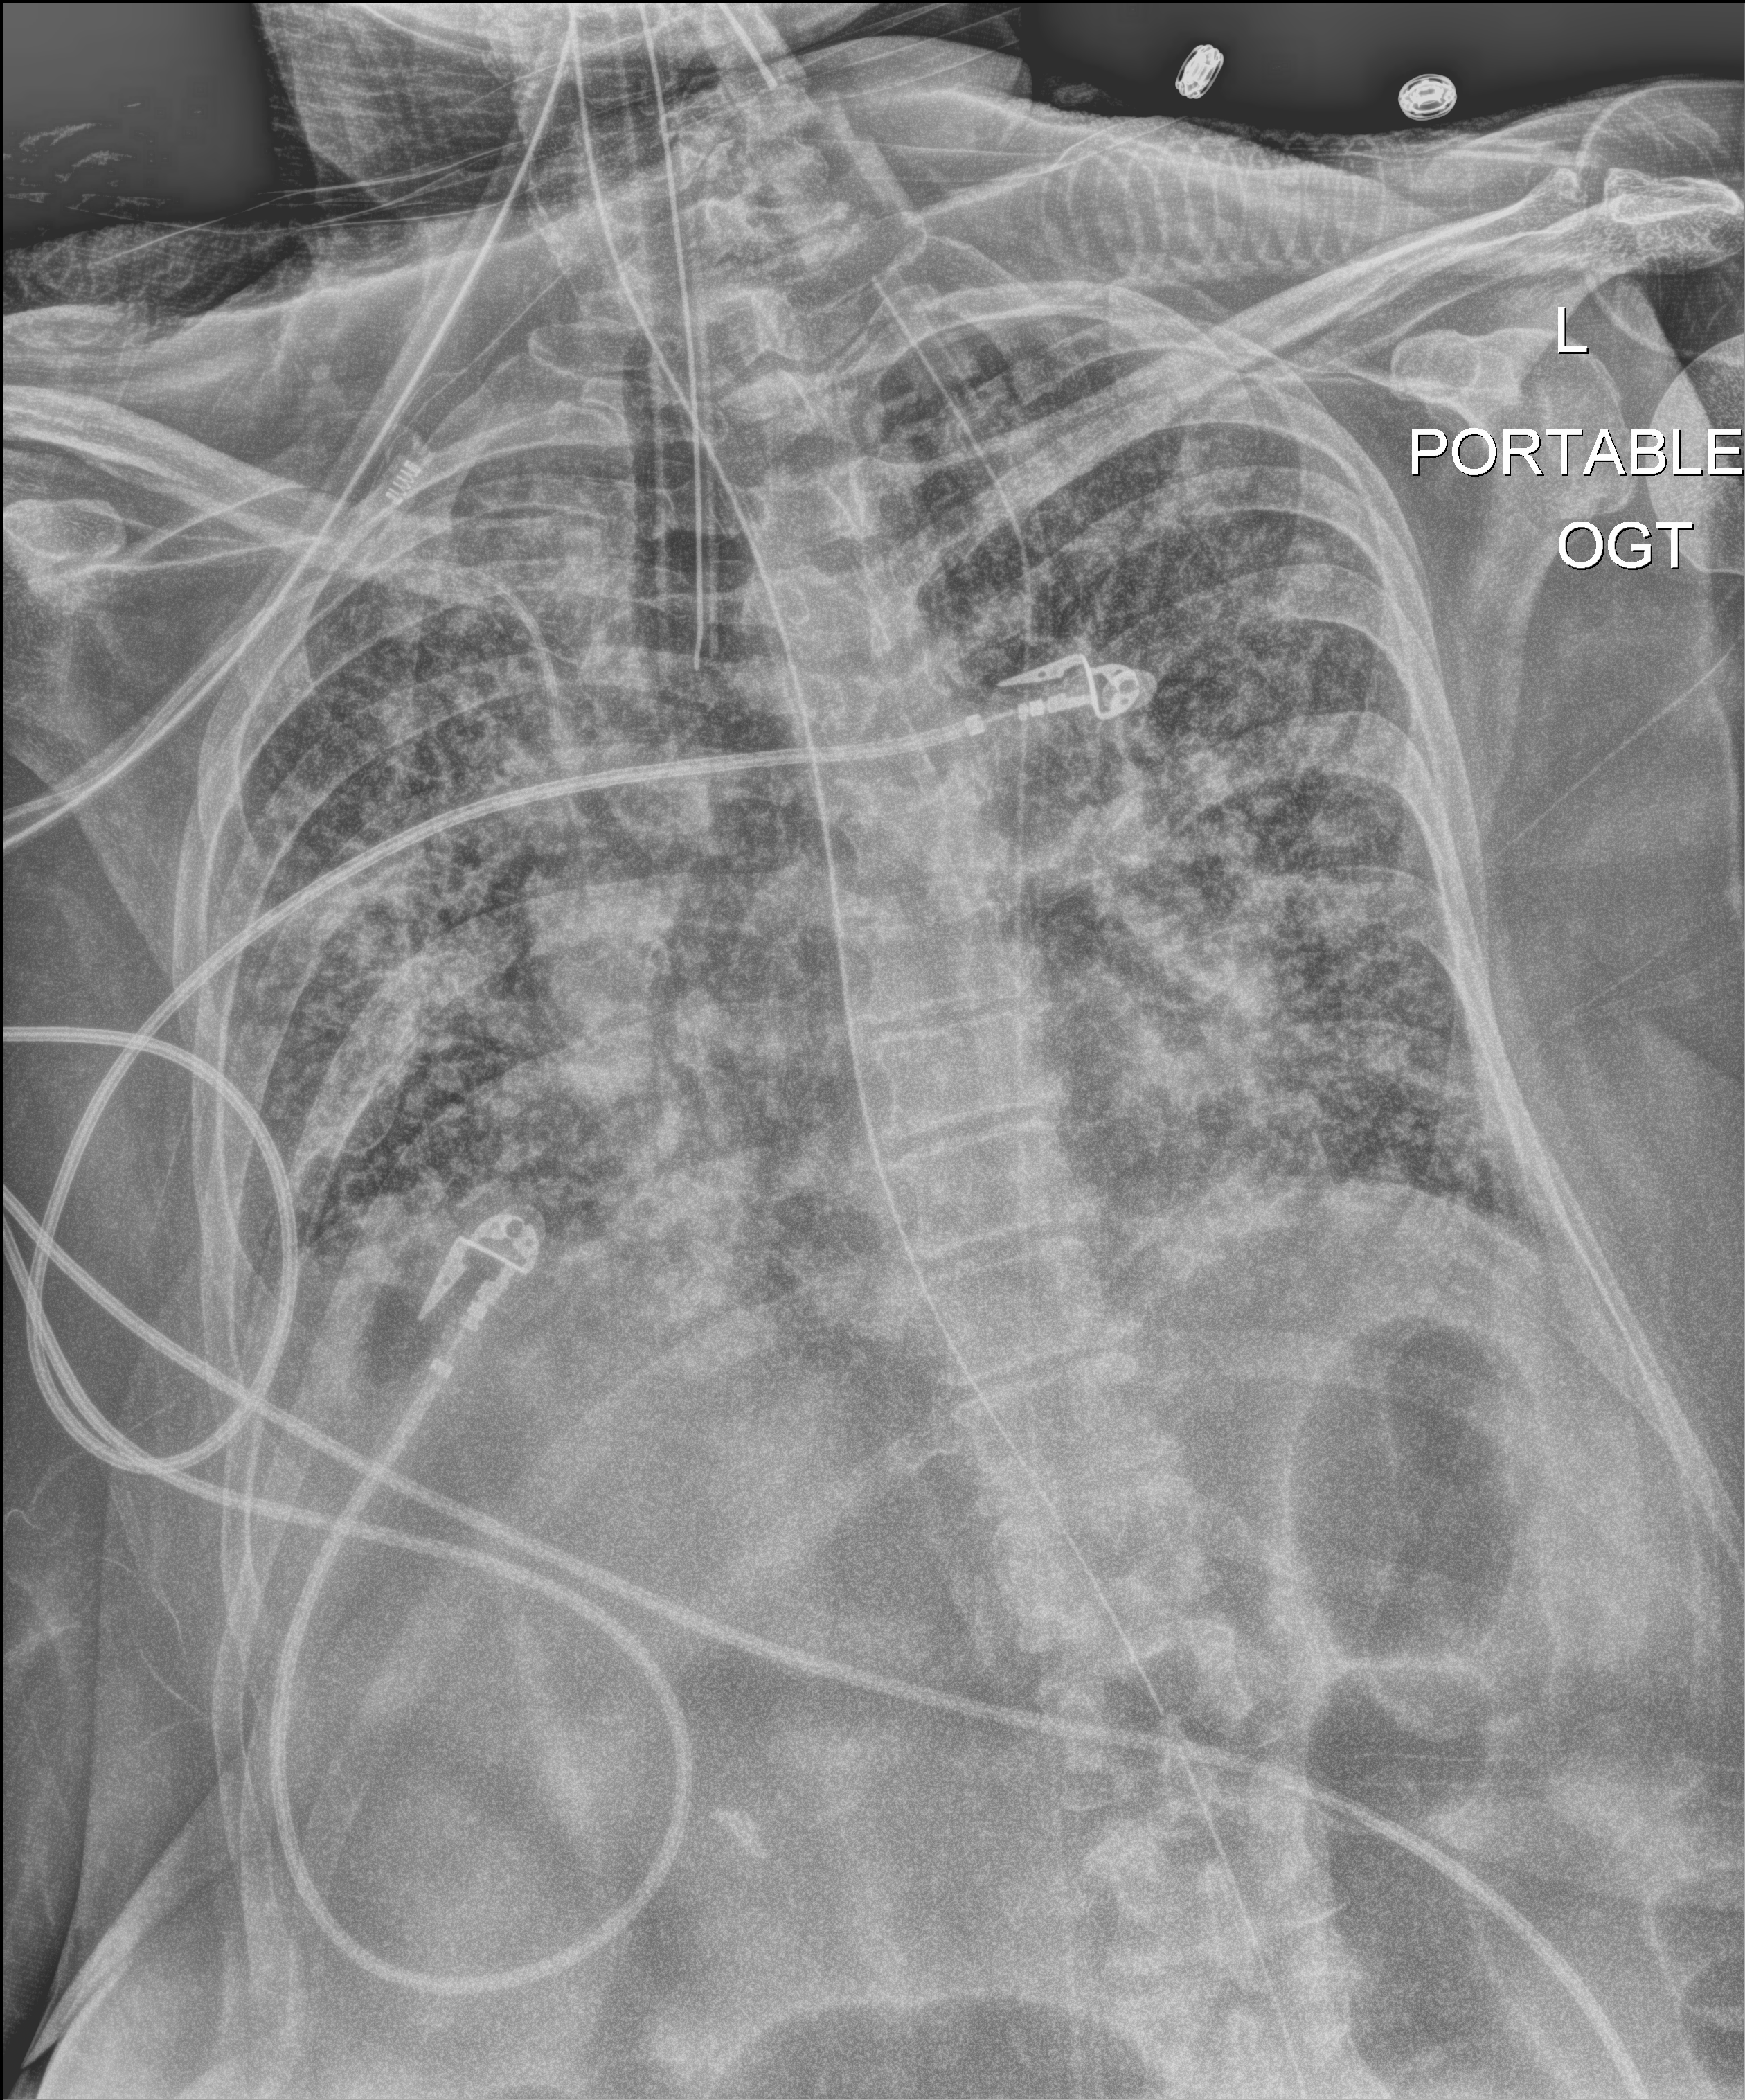
Bedside chest radiograph (digital radiography). Patient hospitalised with COVID-19; female, aged 60–74 years.
From the hospital-stay record, not from the radiograph (when in the stay this image was taken is not recorded):
- hypertension (admission record): yes
- smoking status (admission record): never